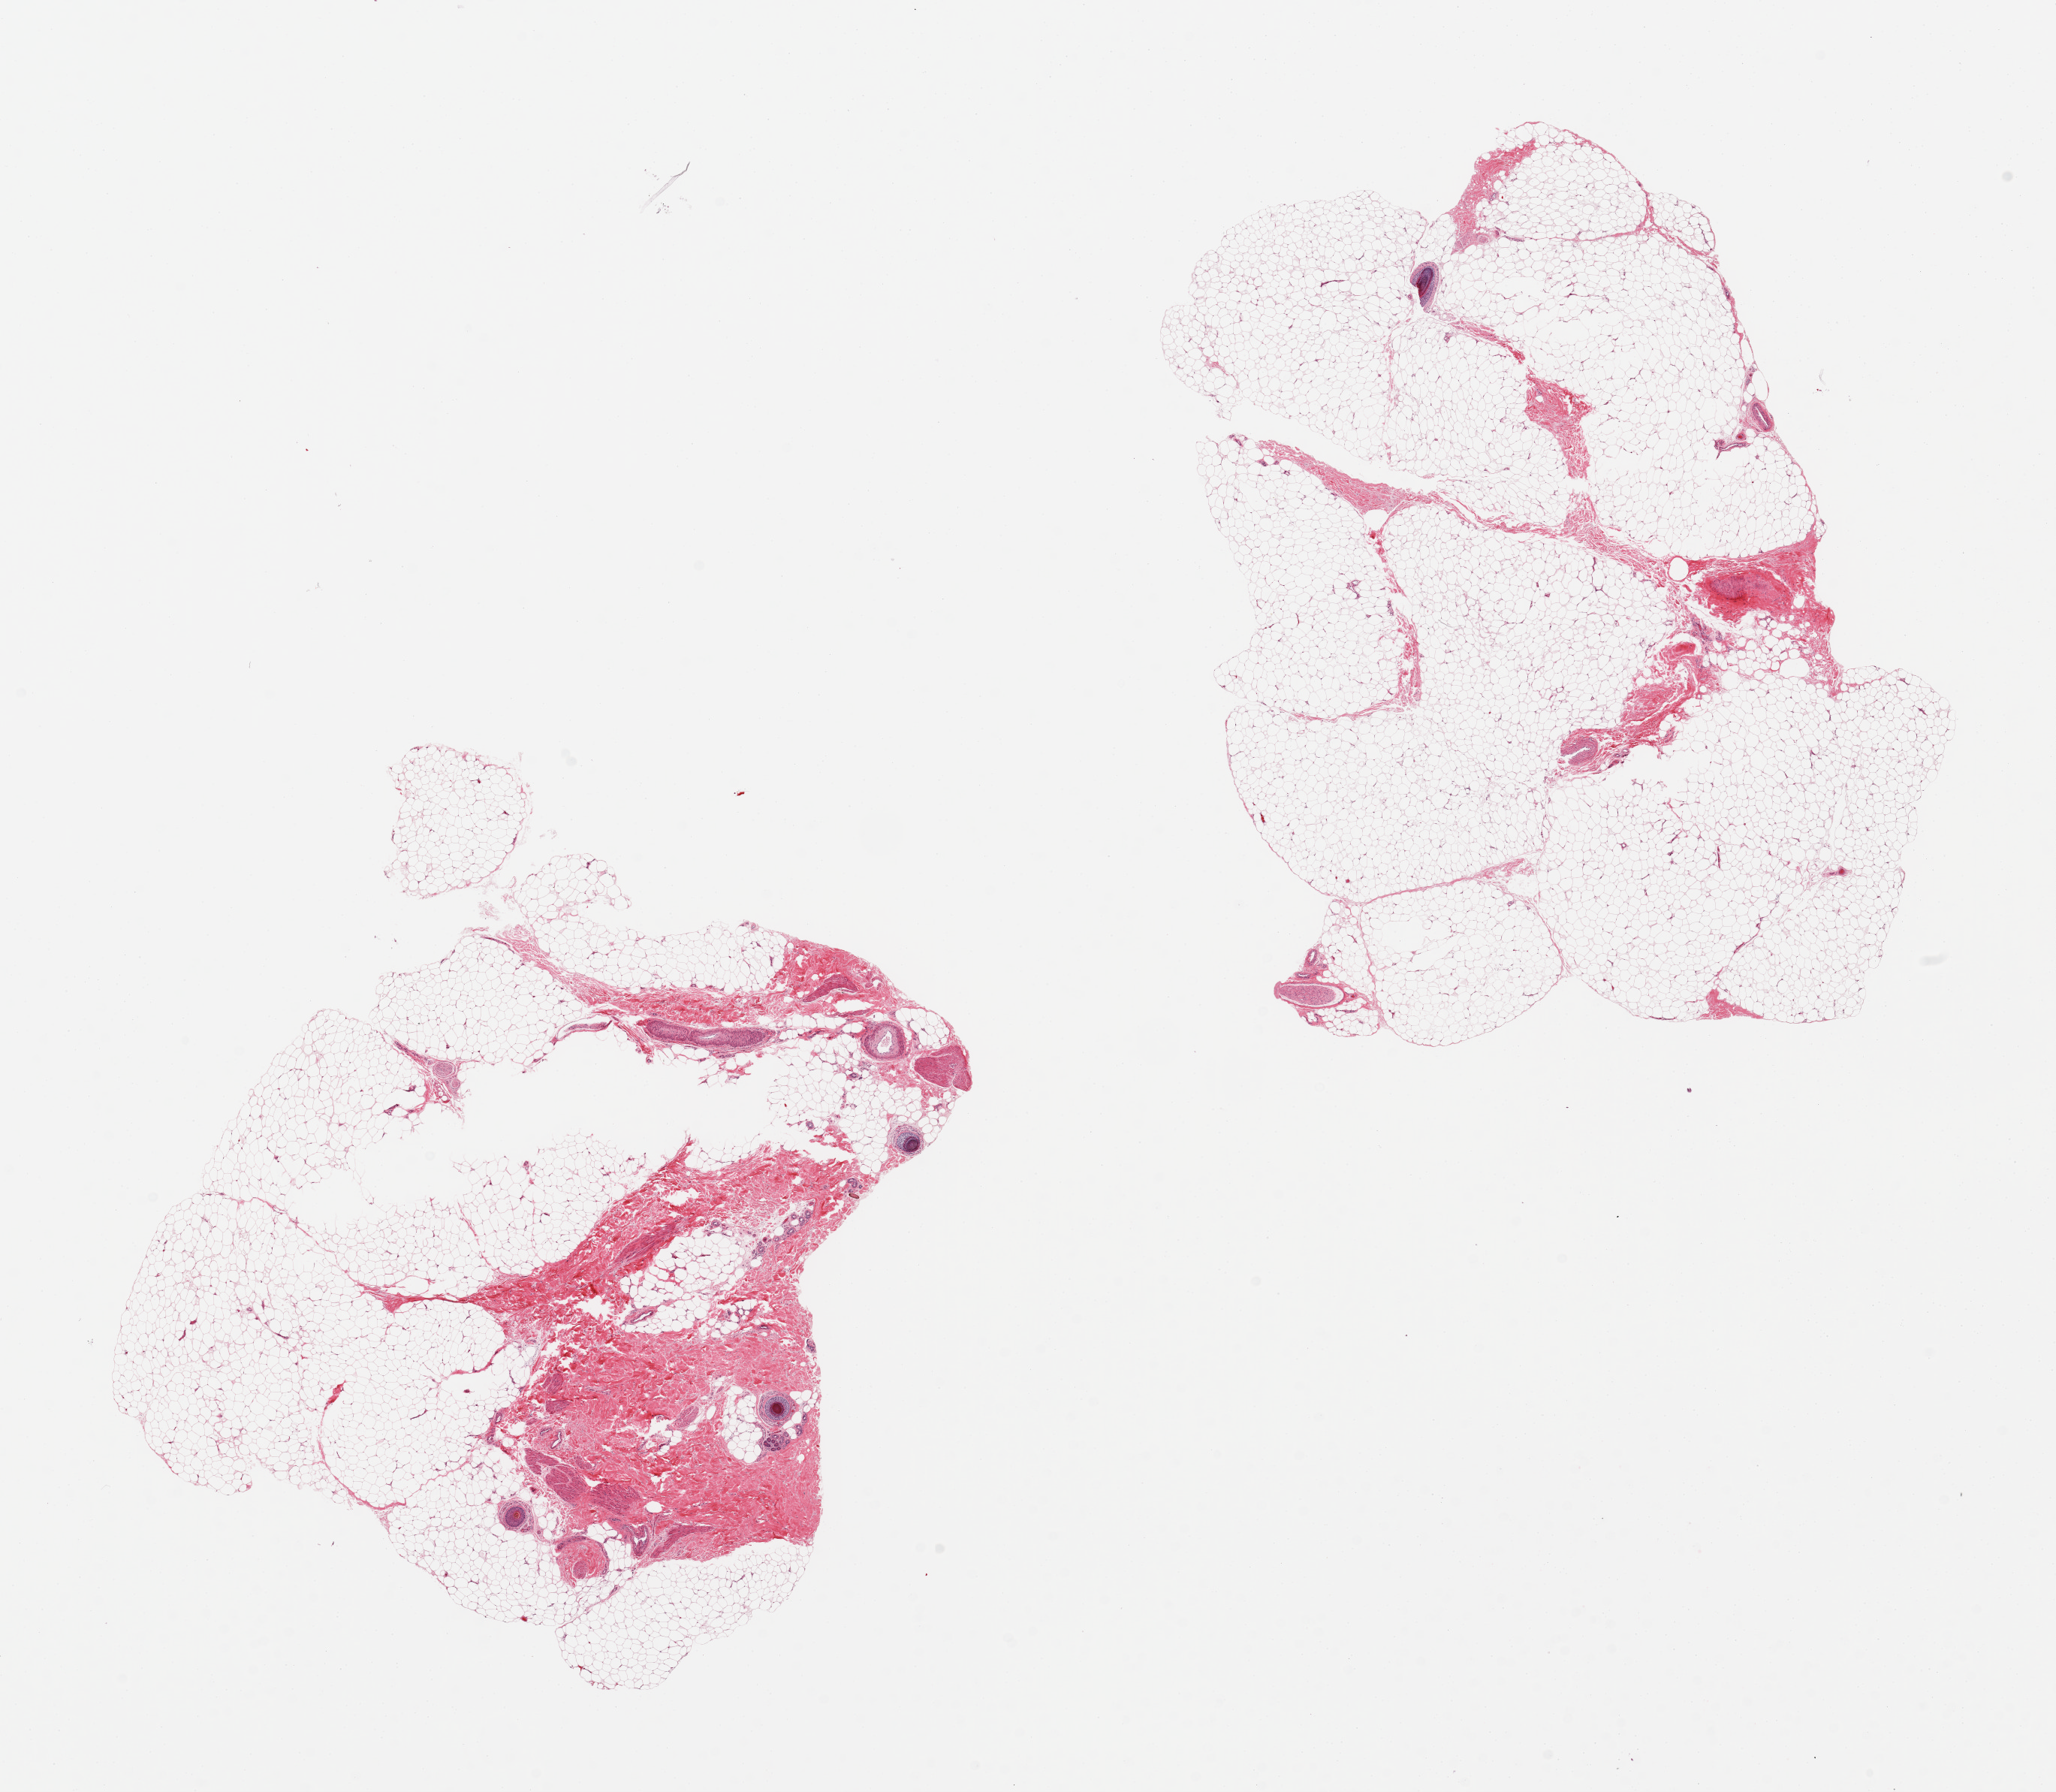
Hematoxylin and eosin (H&E) whole-slide image — whole scanned area (about 21.7 x 18.9 mm, from a 20x scan) shown as a low-resolution overview; PAXgene-fixed paraffin-embedded (PFPE) section; section of adipose tissue (target tissue); donor tissue sample. Donor sex: male.
Reviewer comment on this tissue sample: 2 pieces, one piece includes ~40% fibrous tissue, hair follicles, vessels, sweat glands.